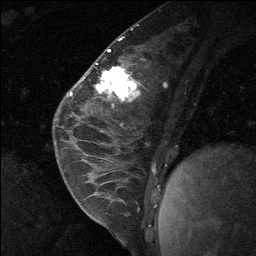
Breast MRI (dynamic contrast-enhanced), one sagittal slice; position 28 of 64 along the scan axis; dynamic contrast-enhanced study with each time point stored as its own series, time point 2 of 3 at this slice position (early post-contrast, ordered by acquisition time); 1.5 T; TE 4.8 ms, TR 27 ms; 2 mm slice thickness; 256 × 256 image matrix, field of view 180 × 180 mm. Female patient, age 26 years. Case-level facts recorded for this patient, not image findings: setting: breast cancer imaged before/during neoadjuvant chemotherapy; receptor status: HR-positive, HER2-negative.
Outlined on this slice (semi-automatic segmentation, software-assisted and operator-edited):
- analysis volume of interest (the breast-tissue region the enhancement analysis was run in; not a lesion): bounding box [x1, y1, x2, y2] px = [86, 43, 127, 137]
- tumour enhancement mask (voxels above the 90 % enhancement threshold inside the analysis volume of interest): [96, 70, 122, 91]